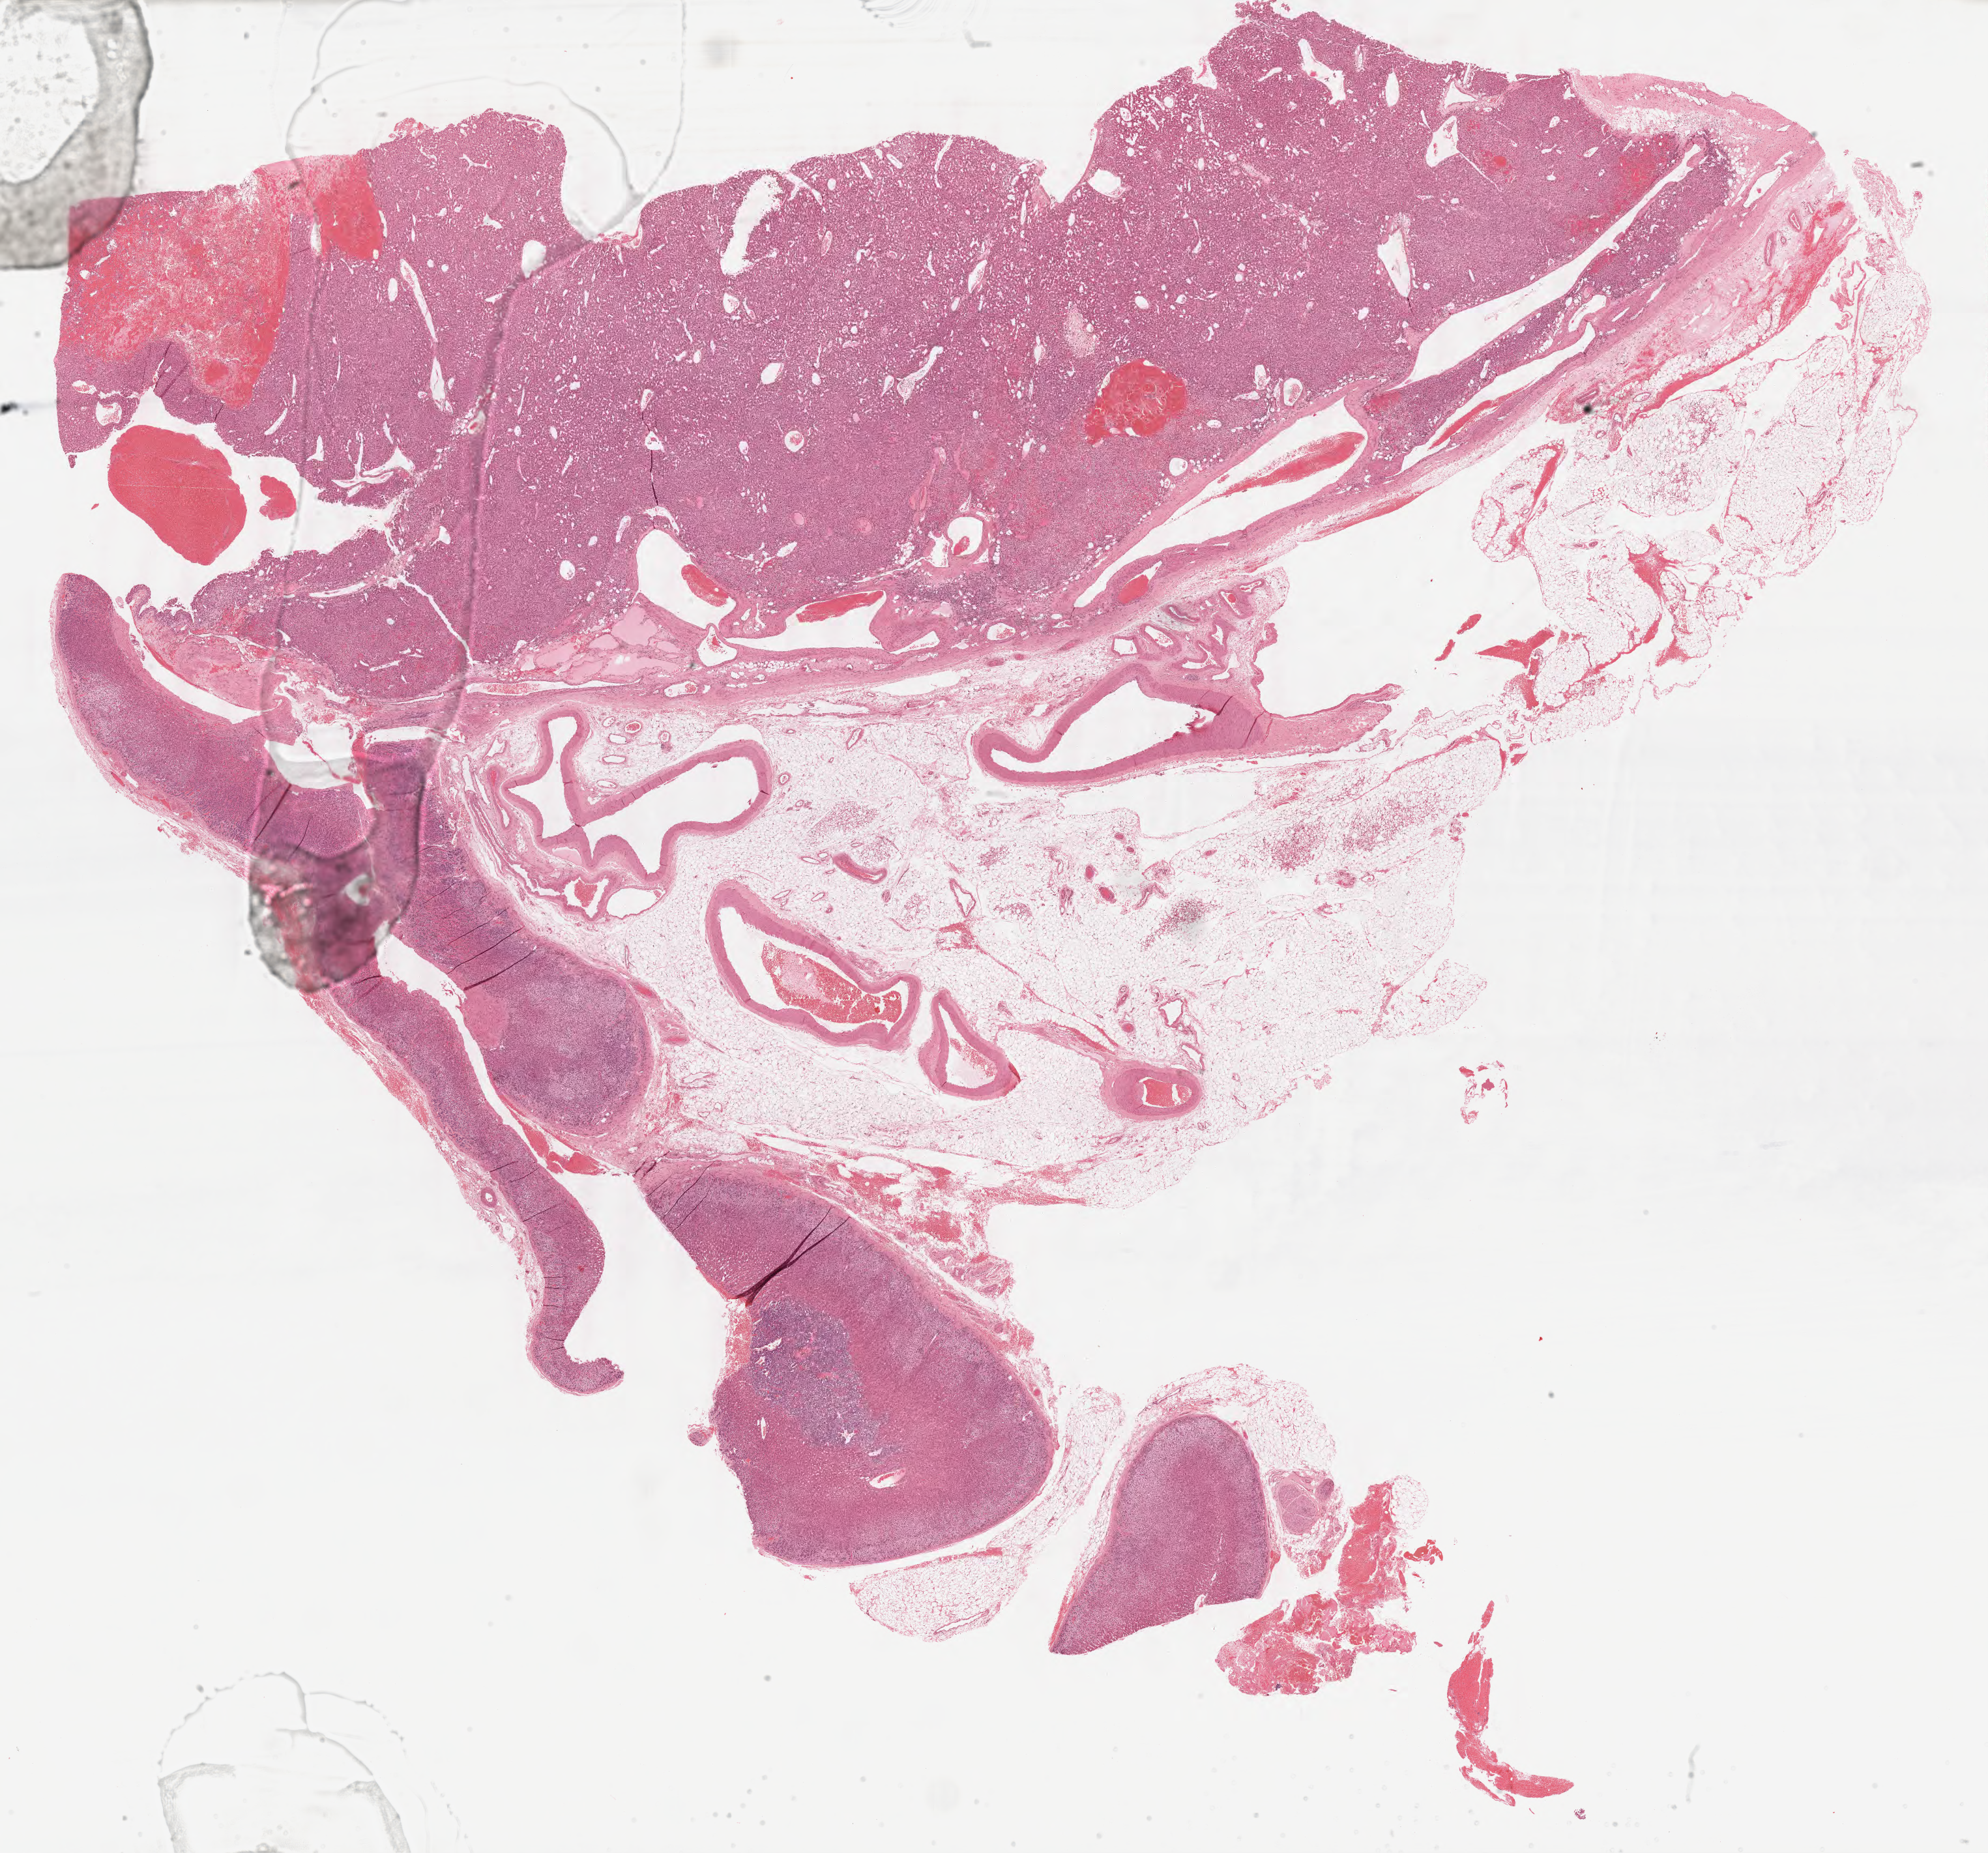
Whole-slide histology image, H&E — a low-resolution overview of the entire scanned area, about 24.1 x 22.5 mm (slide scanned at 40x). Formalin-fixed paraffin-embedded (FFPE) diagnostic section. Adrenal cortex, primary tumour sample. Female patient; age at initial diagnosis 27 years.
Laterality: right. Diagnosis: Adrenal cortical carcinoma (cortex of adrenal gland).